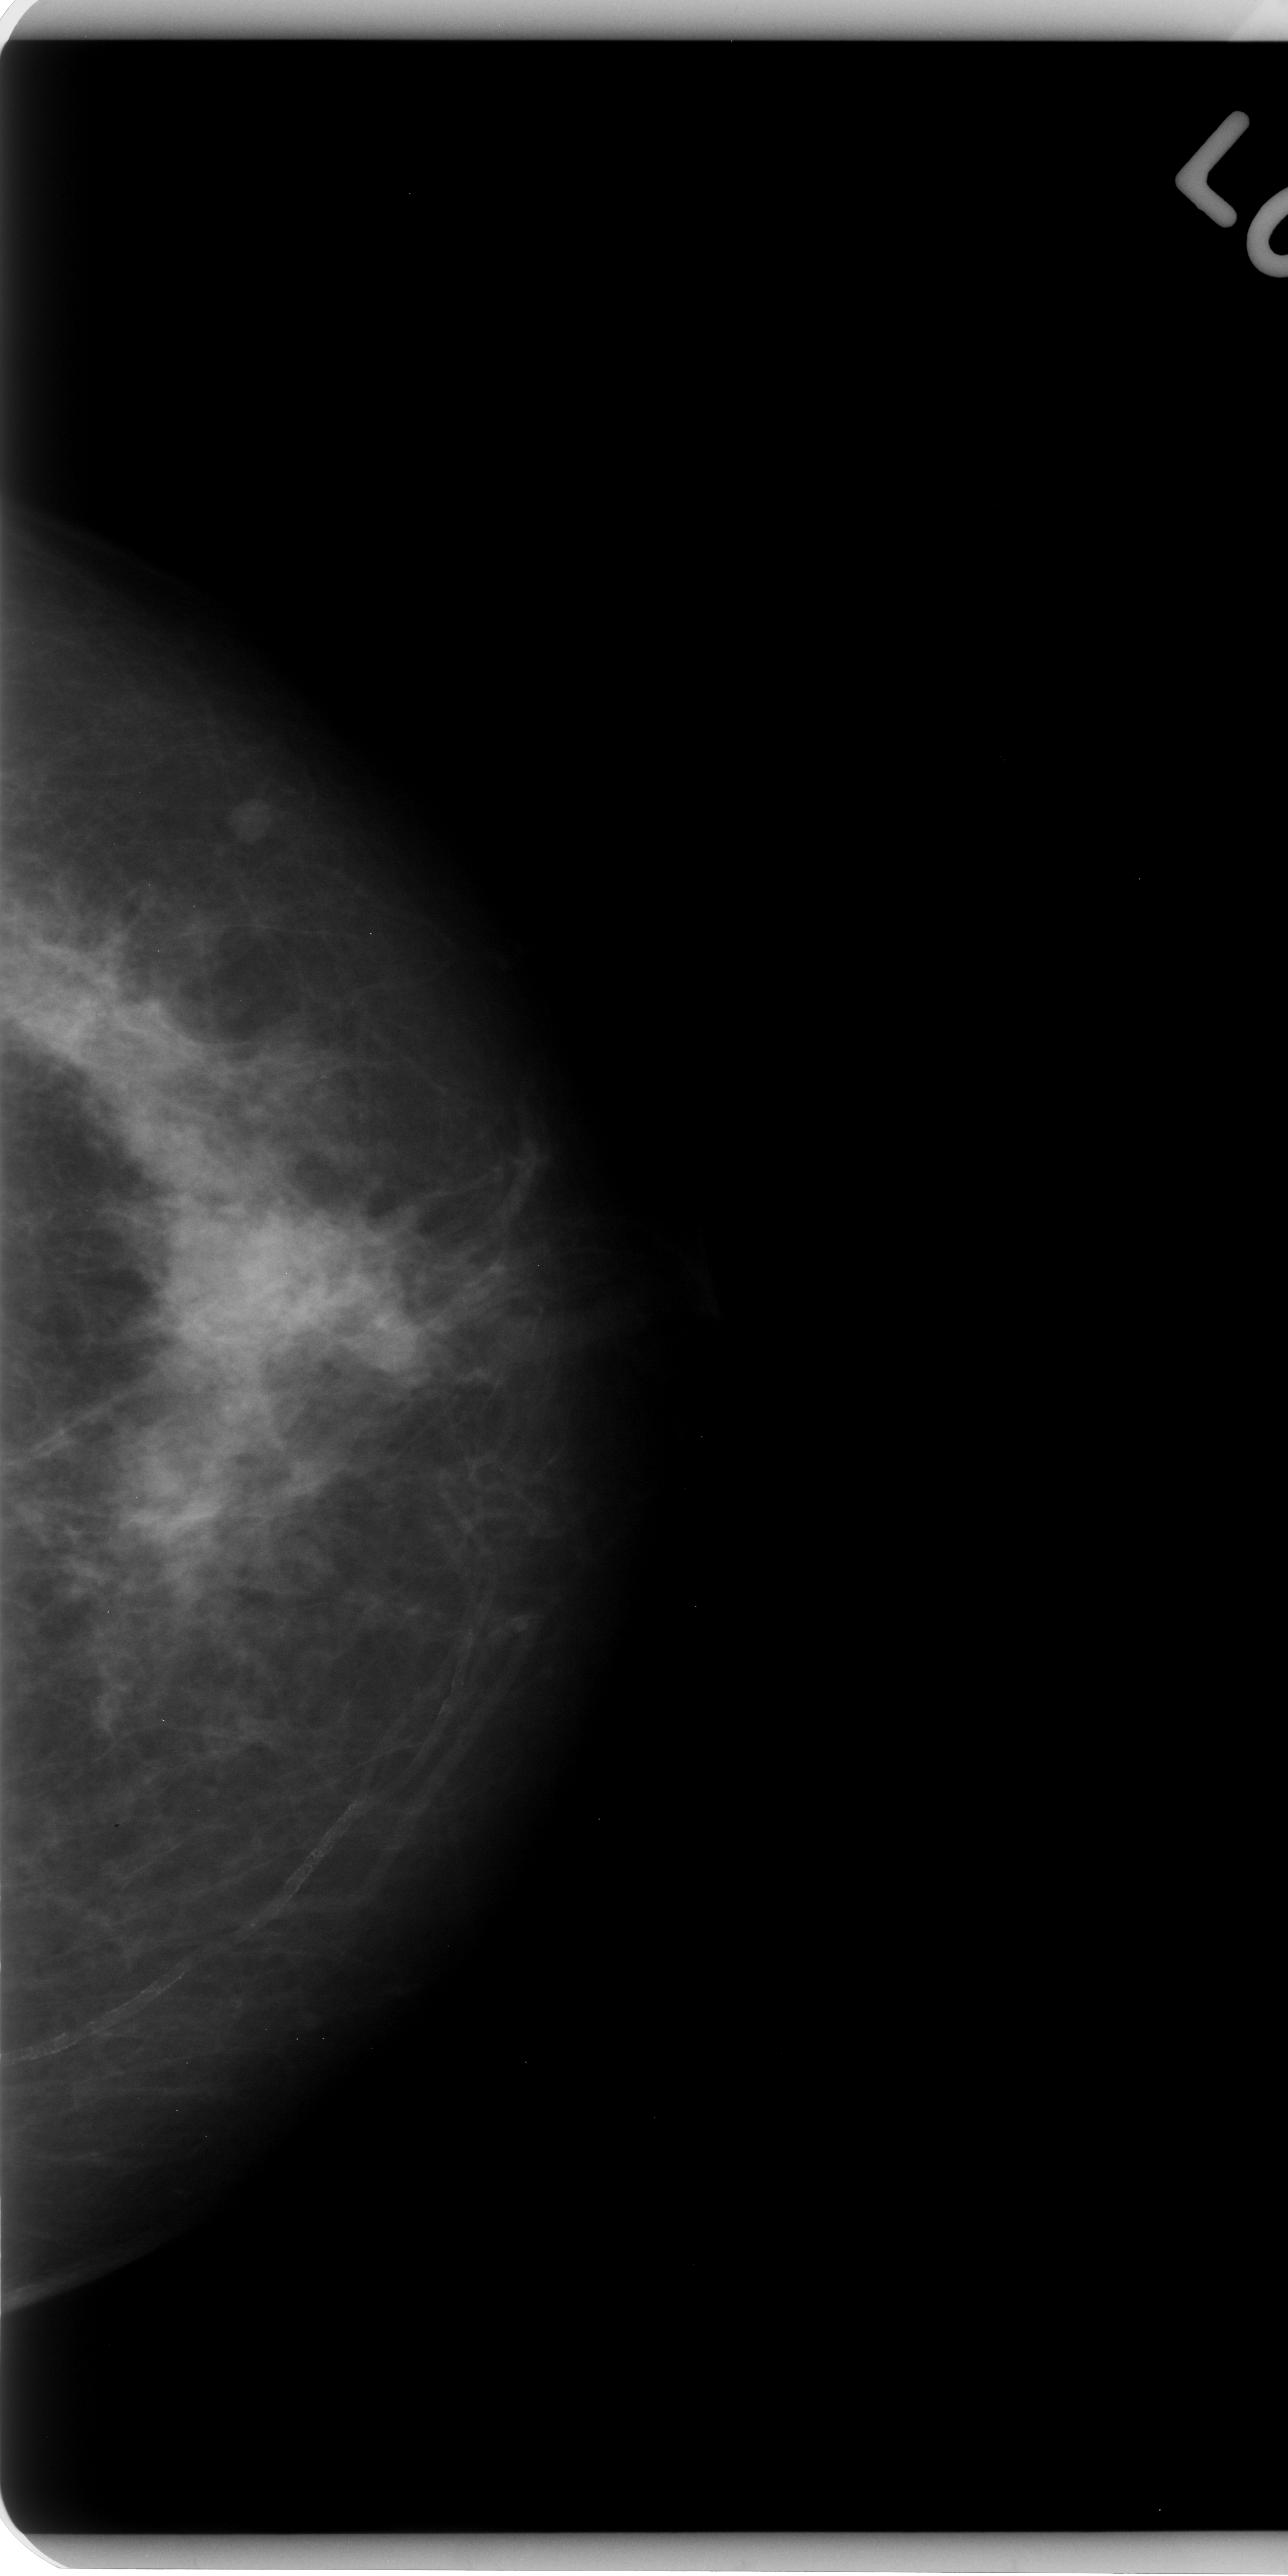
Mammogram (digitized film). Left breast. Craniocaudal (CC) view. Breast composition: scattered fibroglandular densities (BI-RADS density category 2 of 4). 1288 × 2576 image matrix.
Expert-marked regions of interest on this film, with their recorded descriptors:
- mass, shape irregular, margins ill defined; BI-RADS assessment category 4; subtlety rating 2 on a 1 (subtle) to 5 (obvious) scale; pathology result (as recorded, not read from the image): benign: box from (x=191, y=1198) to (x=374, y=1365) px